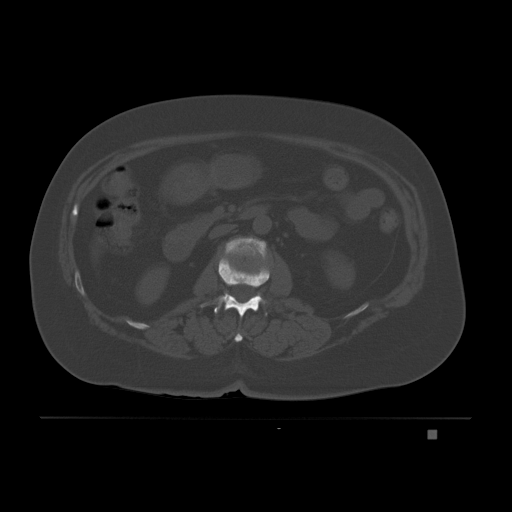
CT including the spine, one axial slice. Slice 69 of 221 in the series (ordered by position). Bone window (W 1800 / L 400 HU). 3 mm slice thickness. 512 × 512 image matrix, field of view 474 × 474 mm. Patient: female, 63 years. Case-level facts recorded for this patient, not image findings: primary cancer: breast.
Structures marked on this image (semi-automatically segmented with operator editing):
- L1 vertebra: bounding box [x1, y1, x2, y2] px = [200, 256, 280, 318]
- L2 vertebra: [224, 237, 267, 262]
- T12 vertebra: [234, 333, 243, 342]